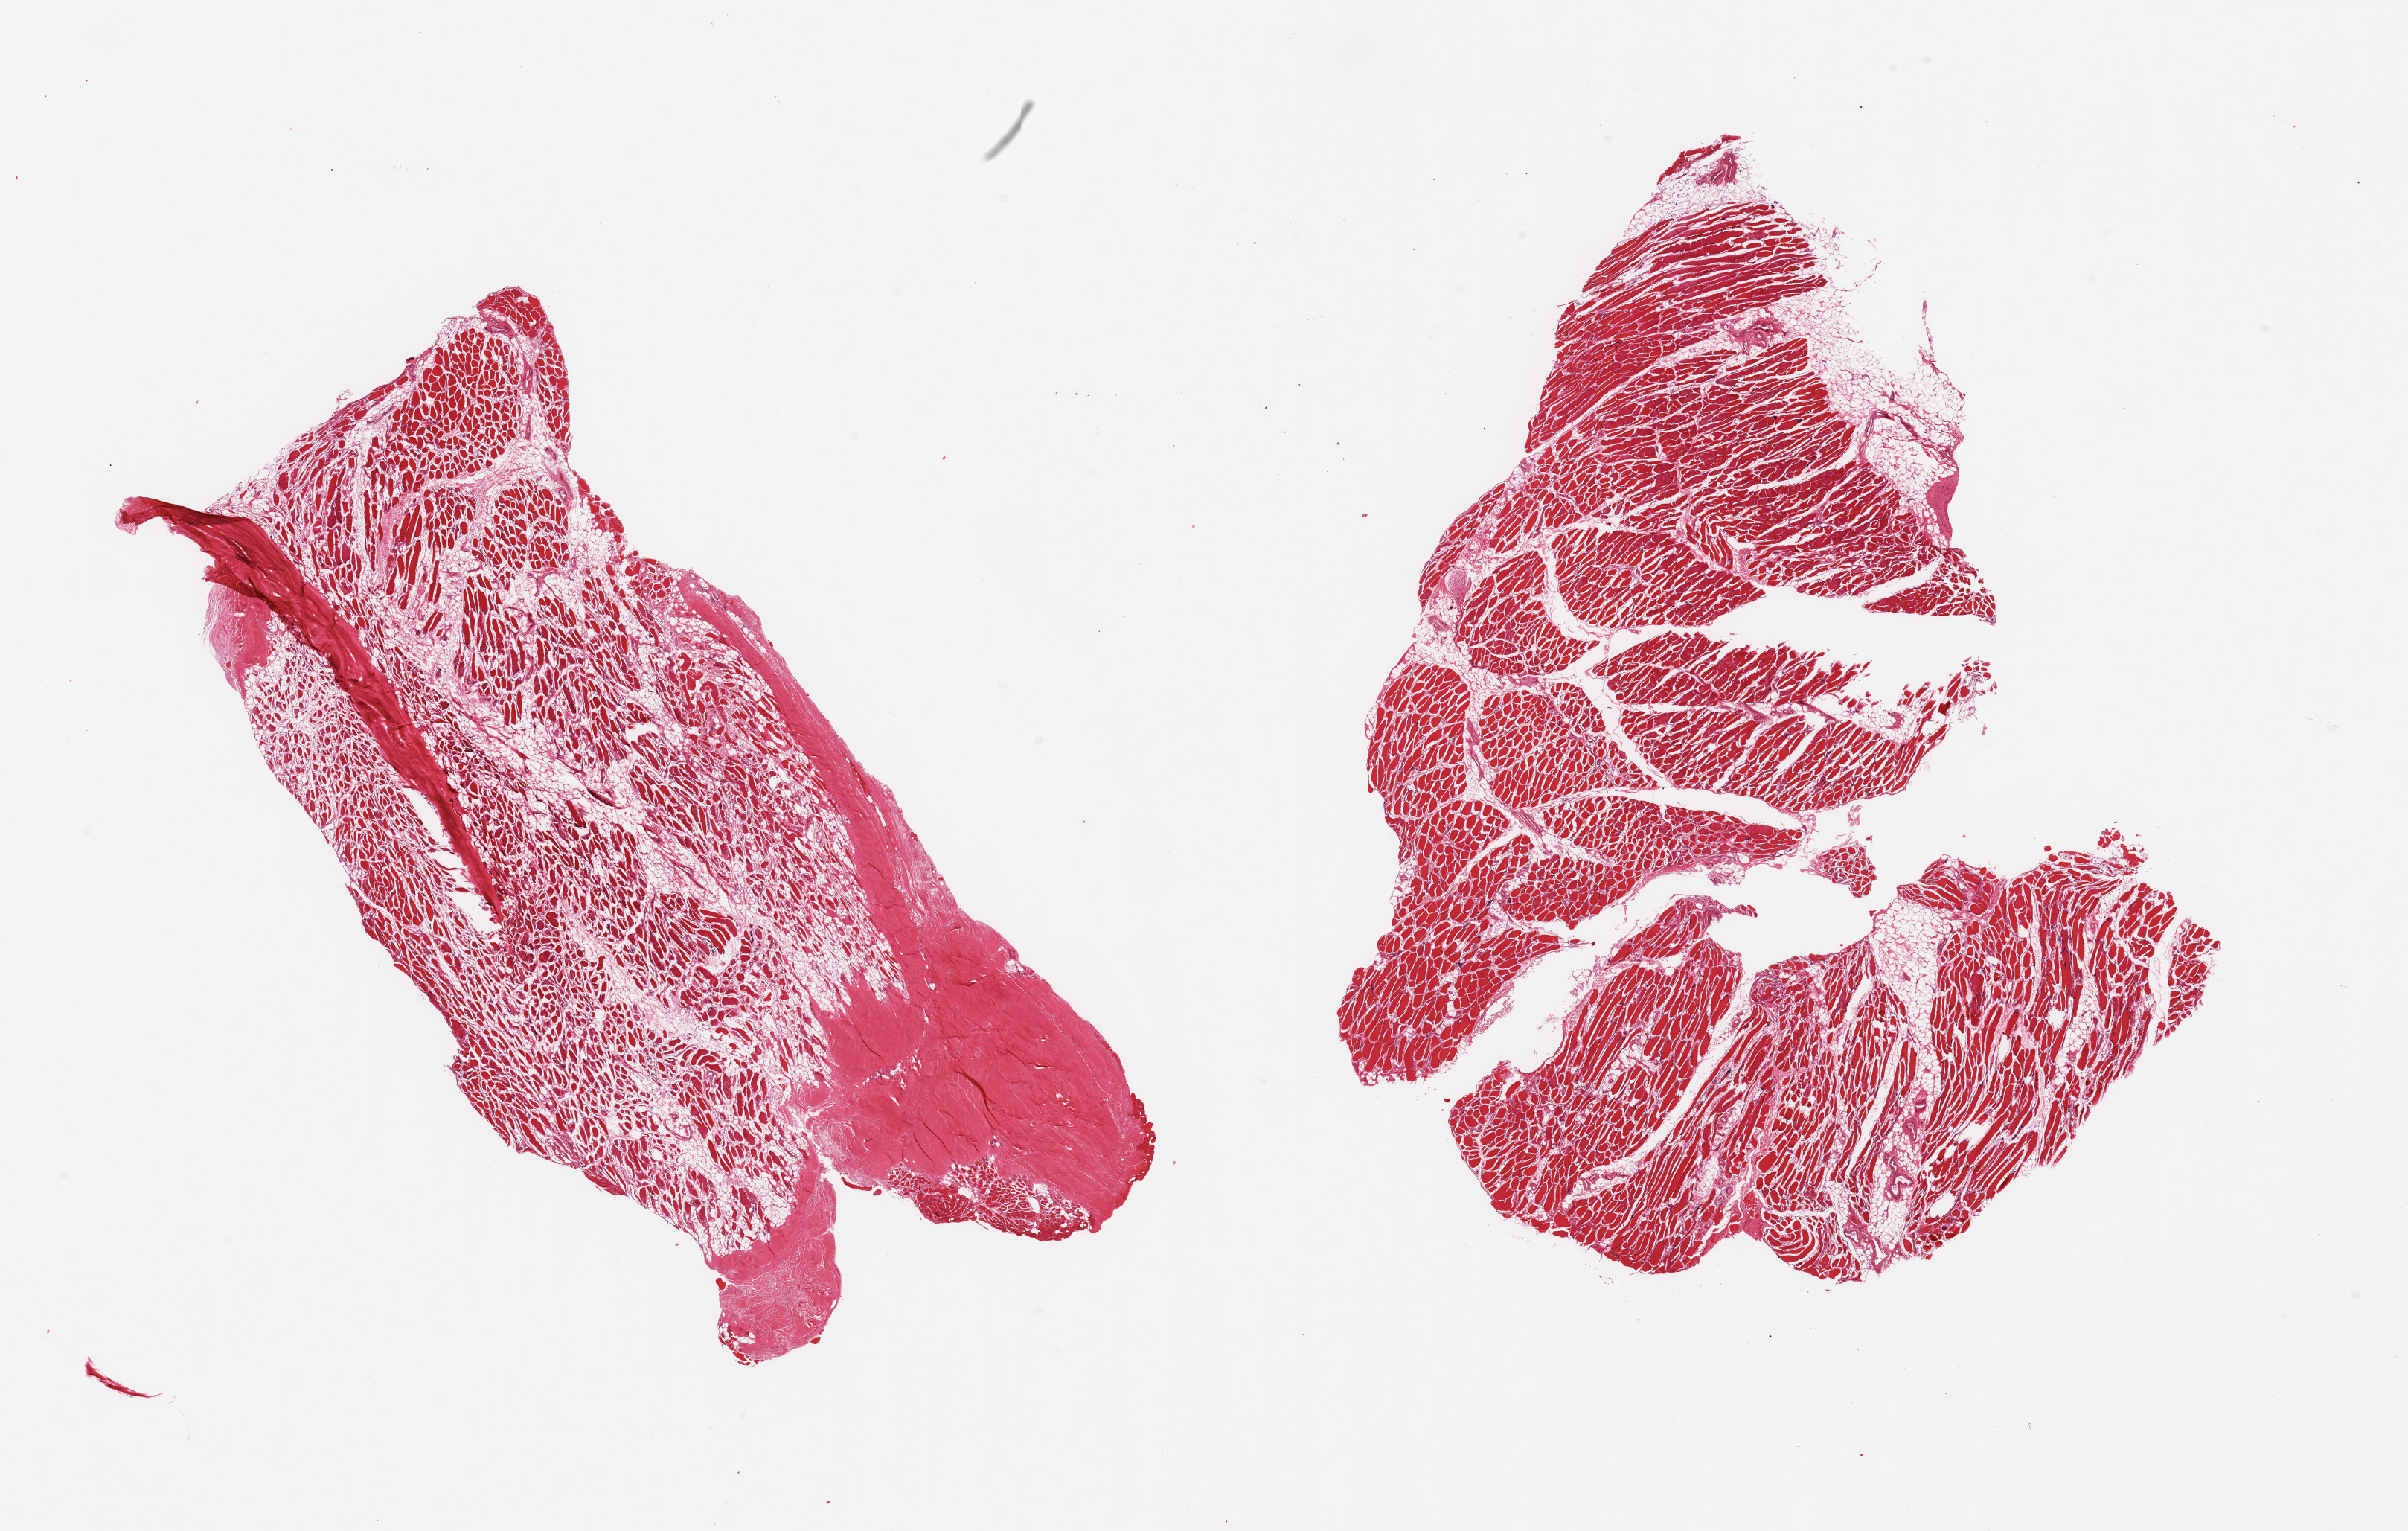
Digitized haematoxylin and eosin-stained section — shown as a low-resolution overview of the whole scanned area (about 25.6 x 16.3 mm, acquisition: 20x scan). PAXgene-fixed, paraffin-embedded tissue. Sampled site (target tissue): skeletal muscle. Tissue donor sample. Donor: female.
Review note (as recorded): 2 pieces; 1 piece contains 25% tendon & 10% fat; other has 10% fat.